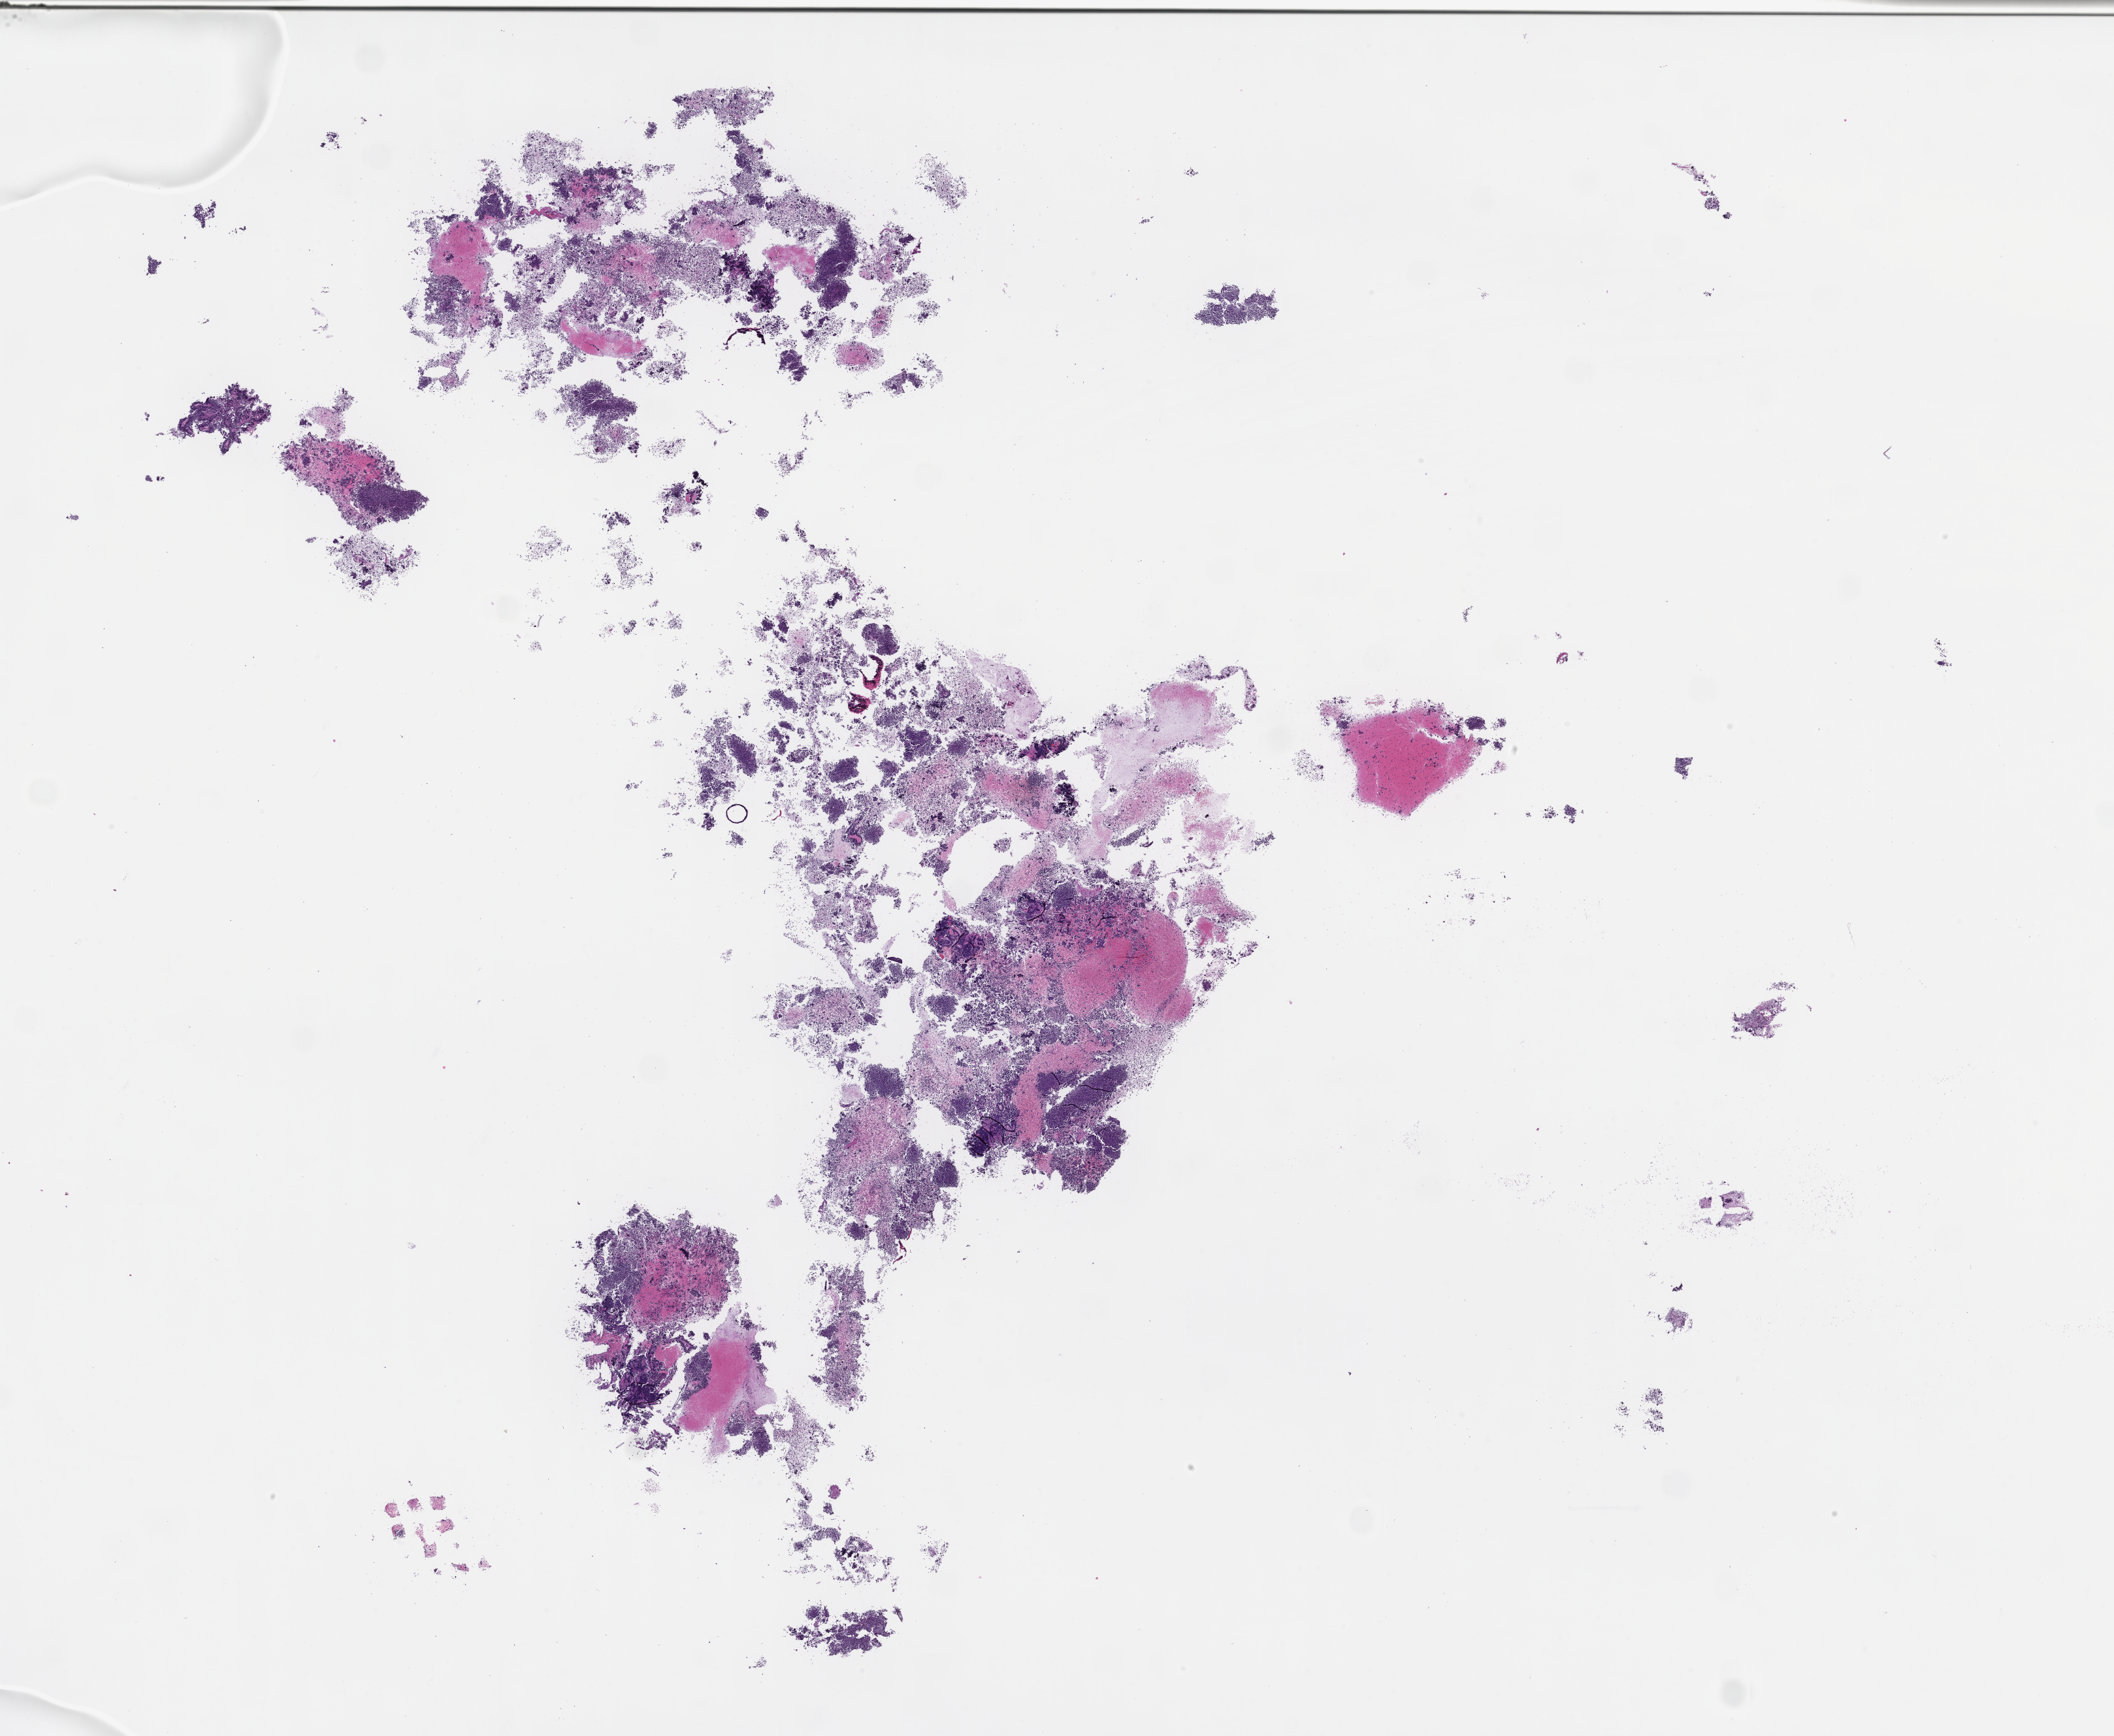
Digitized H&E-stained section — a low-resolution overview of the entire scanned area, about 26.1 x 21.5 mm; formalin-fixed paraffin-embedded section; collected at baseline (before treatment). Patient: male.
This section: metastasis (sampled organ not recorded). Primary diagnosis of the patient: Small Cell Lung Carcinoma.